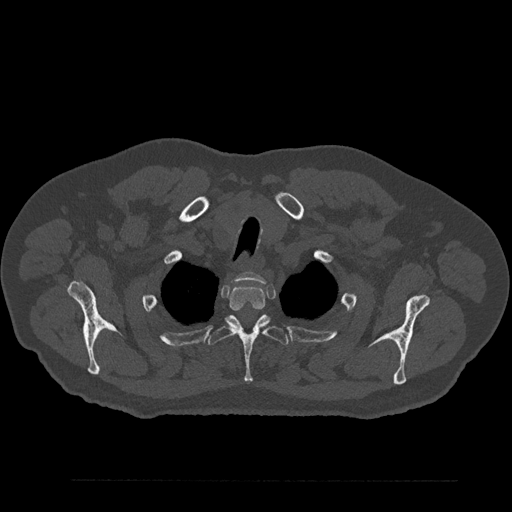
CT including the spine, one axial slice; slice 703 of 797 in the series (ordered by position); 120 kVp; bone window (W 1800 / L 400 HU); 0.5 mm slice thickness; 512 × 512 image matrix, field of view 430 × 430 mm. Patient: male, 61 years. Case-level facts recorded for this patient, not image findings: primary cancer: prostate.
Structures marked on this image (semi-automatic segmentation, software-assisted and operator-edited):
- T1 vertebra: box from (x=236, y=272) to (x=266, y=283) px
- T2 vertebra: (x=229, y=284)–(x=265, y=311)
- T3 vertebra: (x=208, y=314)–(x=289, y=383)